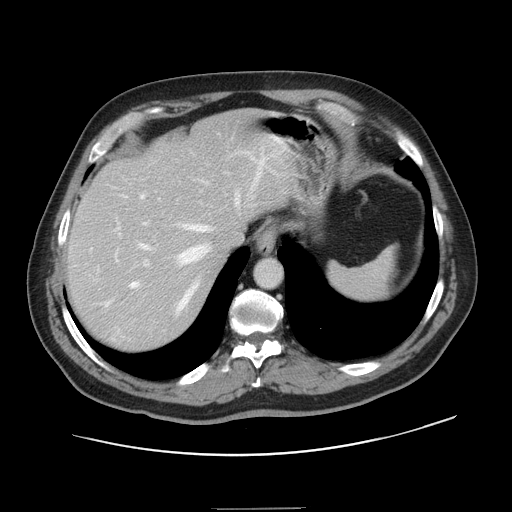
Contrast-enhanced abdominal CT, one axial slice; position 114 of 143 along the scan axis; intravenous contrast given; soft-tissue window (W 400 / L 40 HU); 512 × 512 image matrix, field of view 402 × 402 mm. Male patient, age 62 years. Case-level facts recorded for this patient, not image findings: diagnosis: colorectal cancer liver metastases, imaged before liver resection; multiple liver metastases: yes; largest metastasis: 2.7 cm; disease in both lobes: no.
Structures marked on this image (outlined manually by an expert reader):
- hepatic veins: bounding box (x1, y1, x2, y2) in pixels: (98, 156, 264, 310)
- liver: (68, 114, 295, 352)
- planned liver remnant (the part of the liver to remain after resection): (68, 114, 294, 283)
- portal vein (with intrahepatic branches): (114, 156, 274, 266)